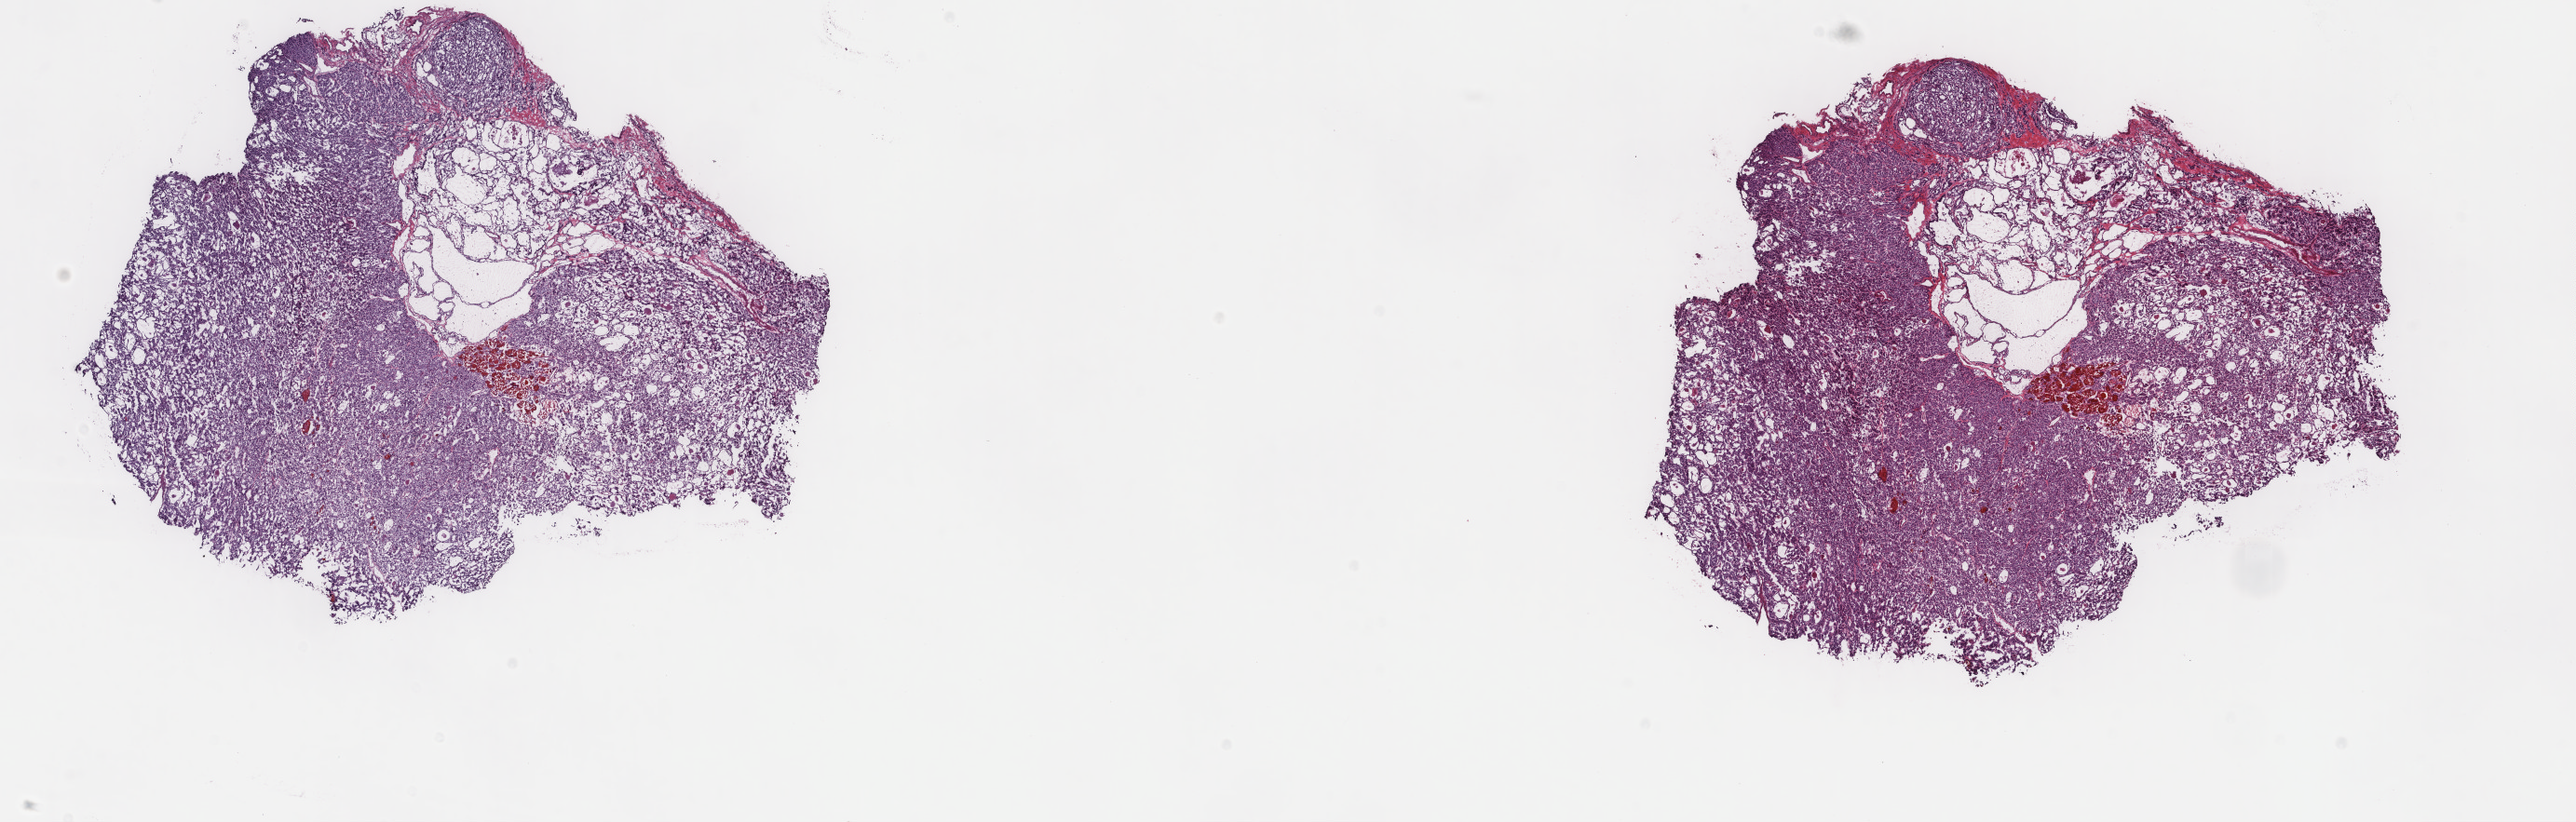
Whole-slide histology image, H&E-stained — shown as a low-resolution overview of the whole scanned area (about 22.0 x 7.0 mm). Frozen section from the top of the tissue portion. Sample: primary tumour, thyroid. Patient: male, age at initial diagnosis 40 years. Slide review estimates, as recorded: tumour cells 80%, tumour nuclei 80%, normal cells 0%, stromal cells 20%, necrosis 0%. Inflammatory infiltration, as recorded: lymphocyte infiltration 2%, monocyte infiltration 0%, neutrophil infiltration 0%.
AJCC pathologic stage: I. Laterality: left. Diagnosis: Papillary carcinoma, follicular variant. Lymph nodes positive (case pathology): 0 of 1 examined.